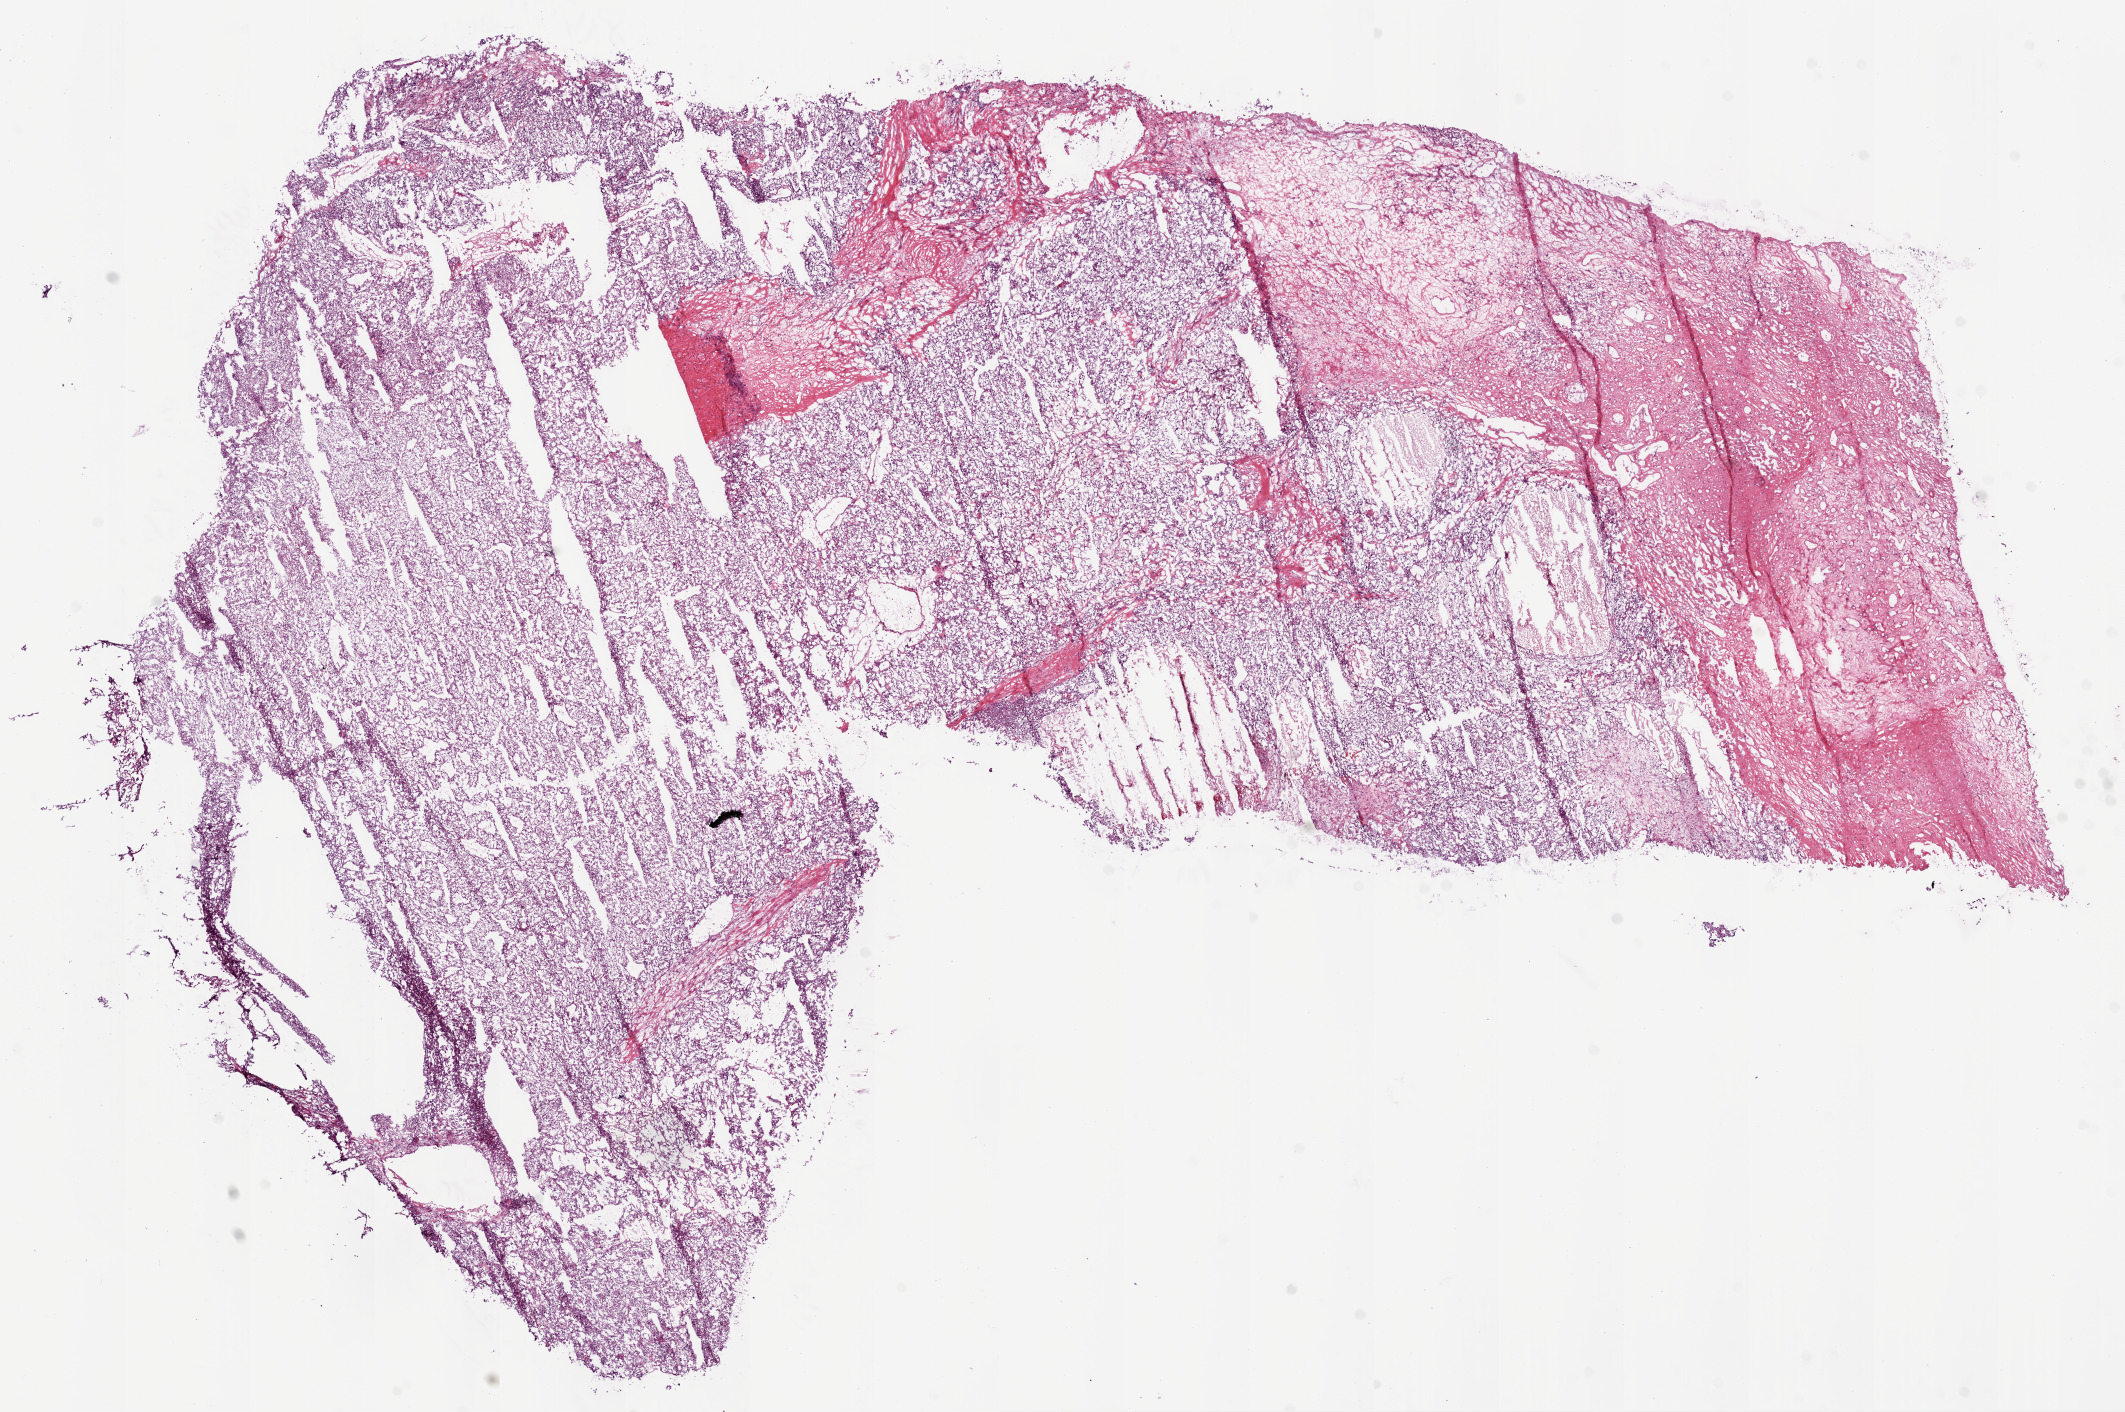
Hematoxylin and eosin (H&E) stained whole-slide image — shown as a low-resolution overview of the whole scanned area (about 17.1 x 11.3 mm, acquisition: 20x scan). Frozen section from the top of the tissue portion. Sample: primary tumour, kidney. Male, age 63 years at initial diagnosis. Histologic grade: G3 (poorly differentiated). Pathologist review of this section (percent, as recorded): tumour cells 75%, tumour nuclei 80%, normal cells 0%, stromal cells 25%, necrosis 0%.
AJCC pathologic stage: I. Histologic diagnosis: Clear cell adenocarcinoma, NOS. Laterality: left.